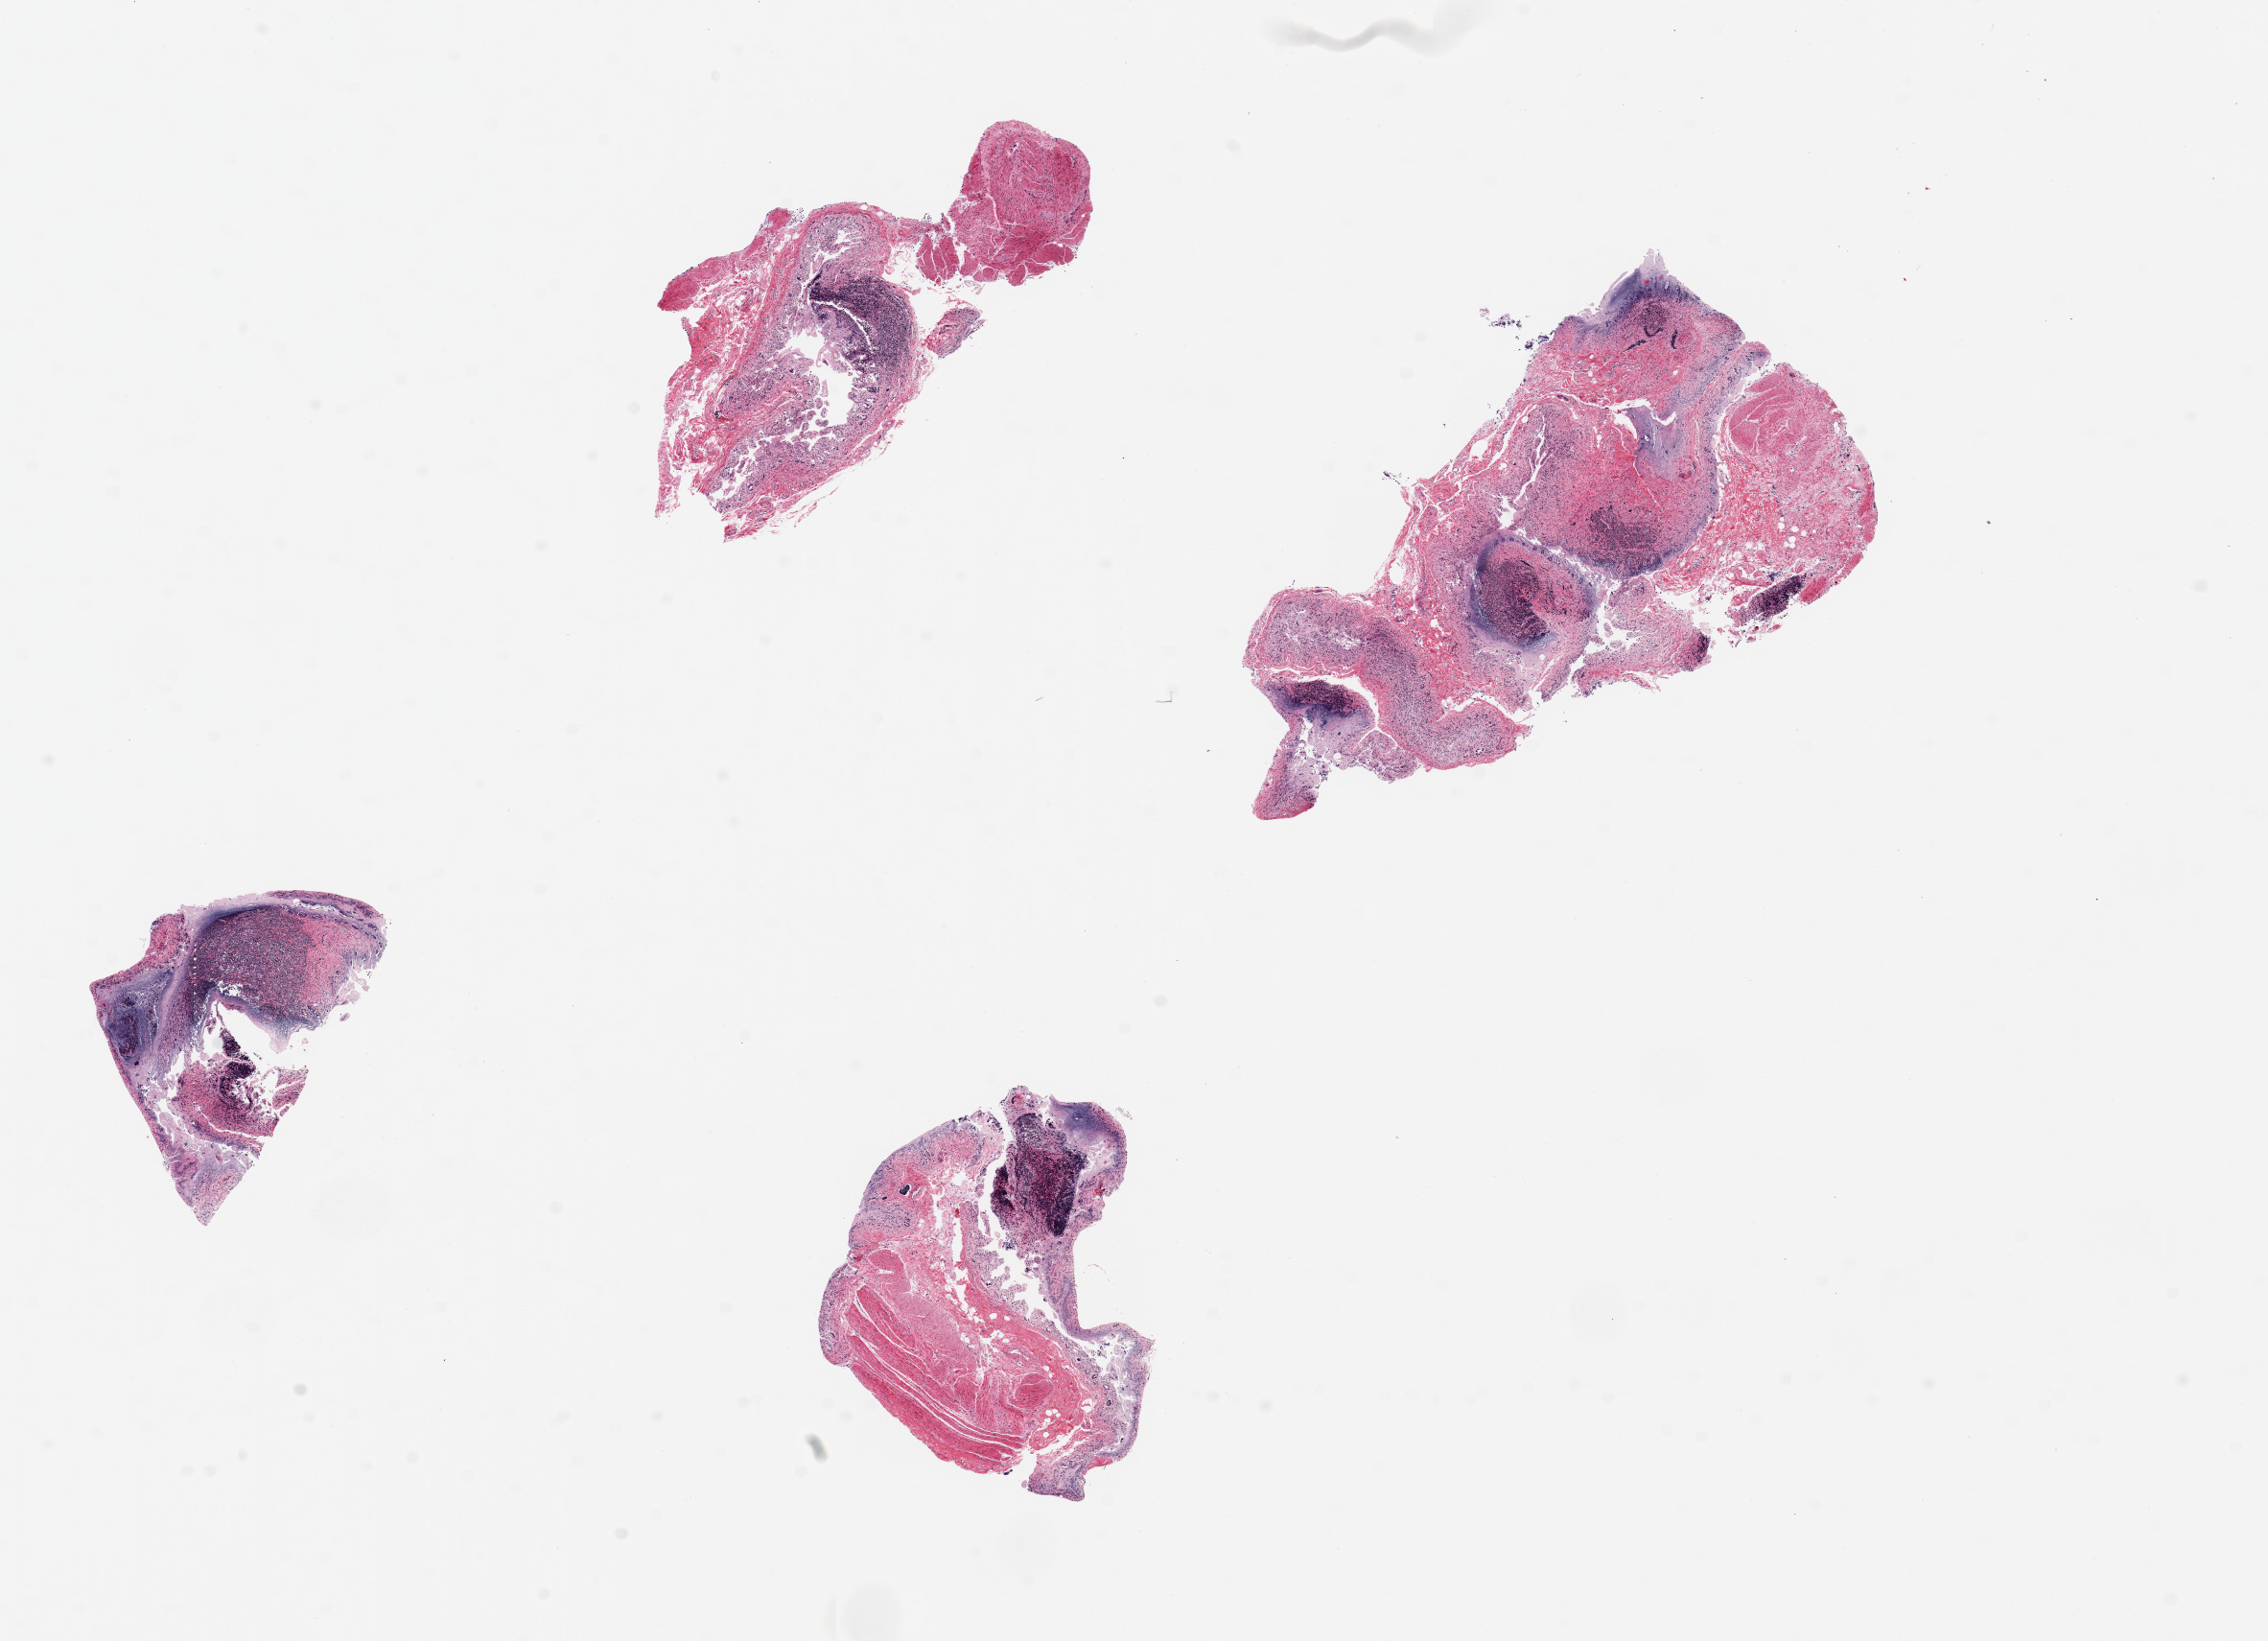
Whole-slide image, hematoxylin and eosin (H&E) stain, brightfield — a low-resolution overview of the entire scanned area, about 18.7 x 13.5 mm (from a 20x scan). PAXgene-fixed, paraffin-embedded tissue. Section of ileum (target tissue). Tissue donor sample.
Pathologist's review note for this sample: p4 ieces ~6x3mm though variably sized; mucoa completely autolyzed, prominent surviving lymphoid aggregates present, deliniated (representative).